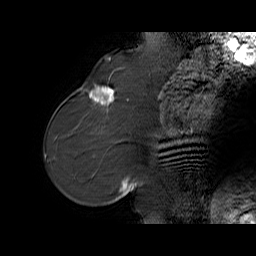
Breast MRI (dynamic contrast-enhanced), one sagittal slice. Slice 22 of 65 in the series (ordered by position). Dynamic contrast-enhanced series, time point 2 of 6 at this slice position (early post-contrast). 1.5 T. TE 5.7 ms, TR 32.9 ms. 4 mm slice thickness. 256 × 256 image matrix, field of view 230 × 230 mm. Female patient. From the clinical record (not read from this slice): setting: breast cancer imaged before/during neoadjuvant chemotherapy; receptor status: HER2-positive.
Outlined on this slice (semi-automatically segmented with operator editing):
- analysis volume of interest (the breast-tissue region the enhancement analysis was run in; not a lesion): box from (x=76, y=77) to (x=125, y=128) px
- tumour enhancement mask (voxels above the 100 % enhancement threshold inside the analysis volume of interest): (x=89, y=86)–(x=115, y=105)